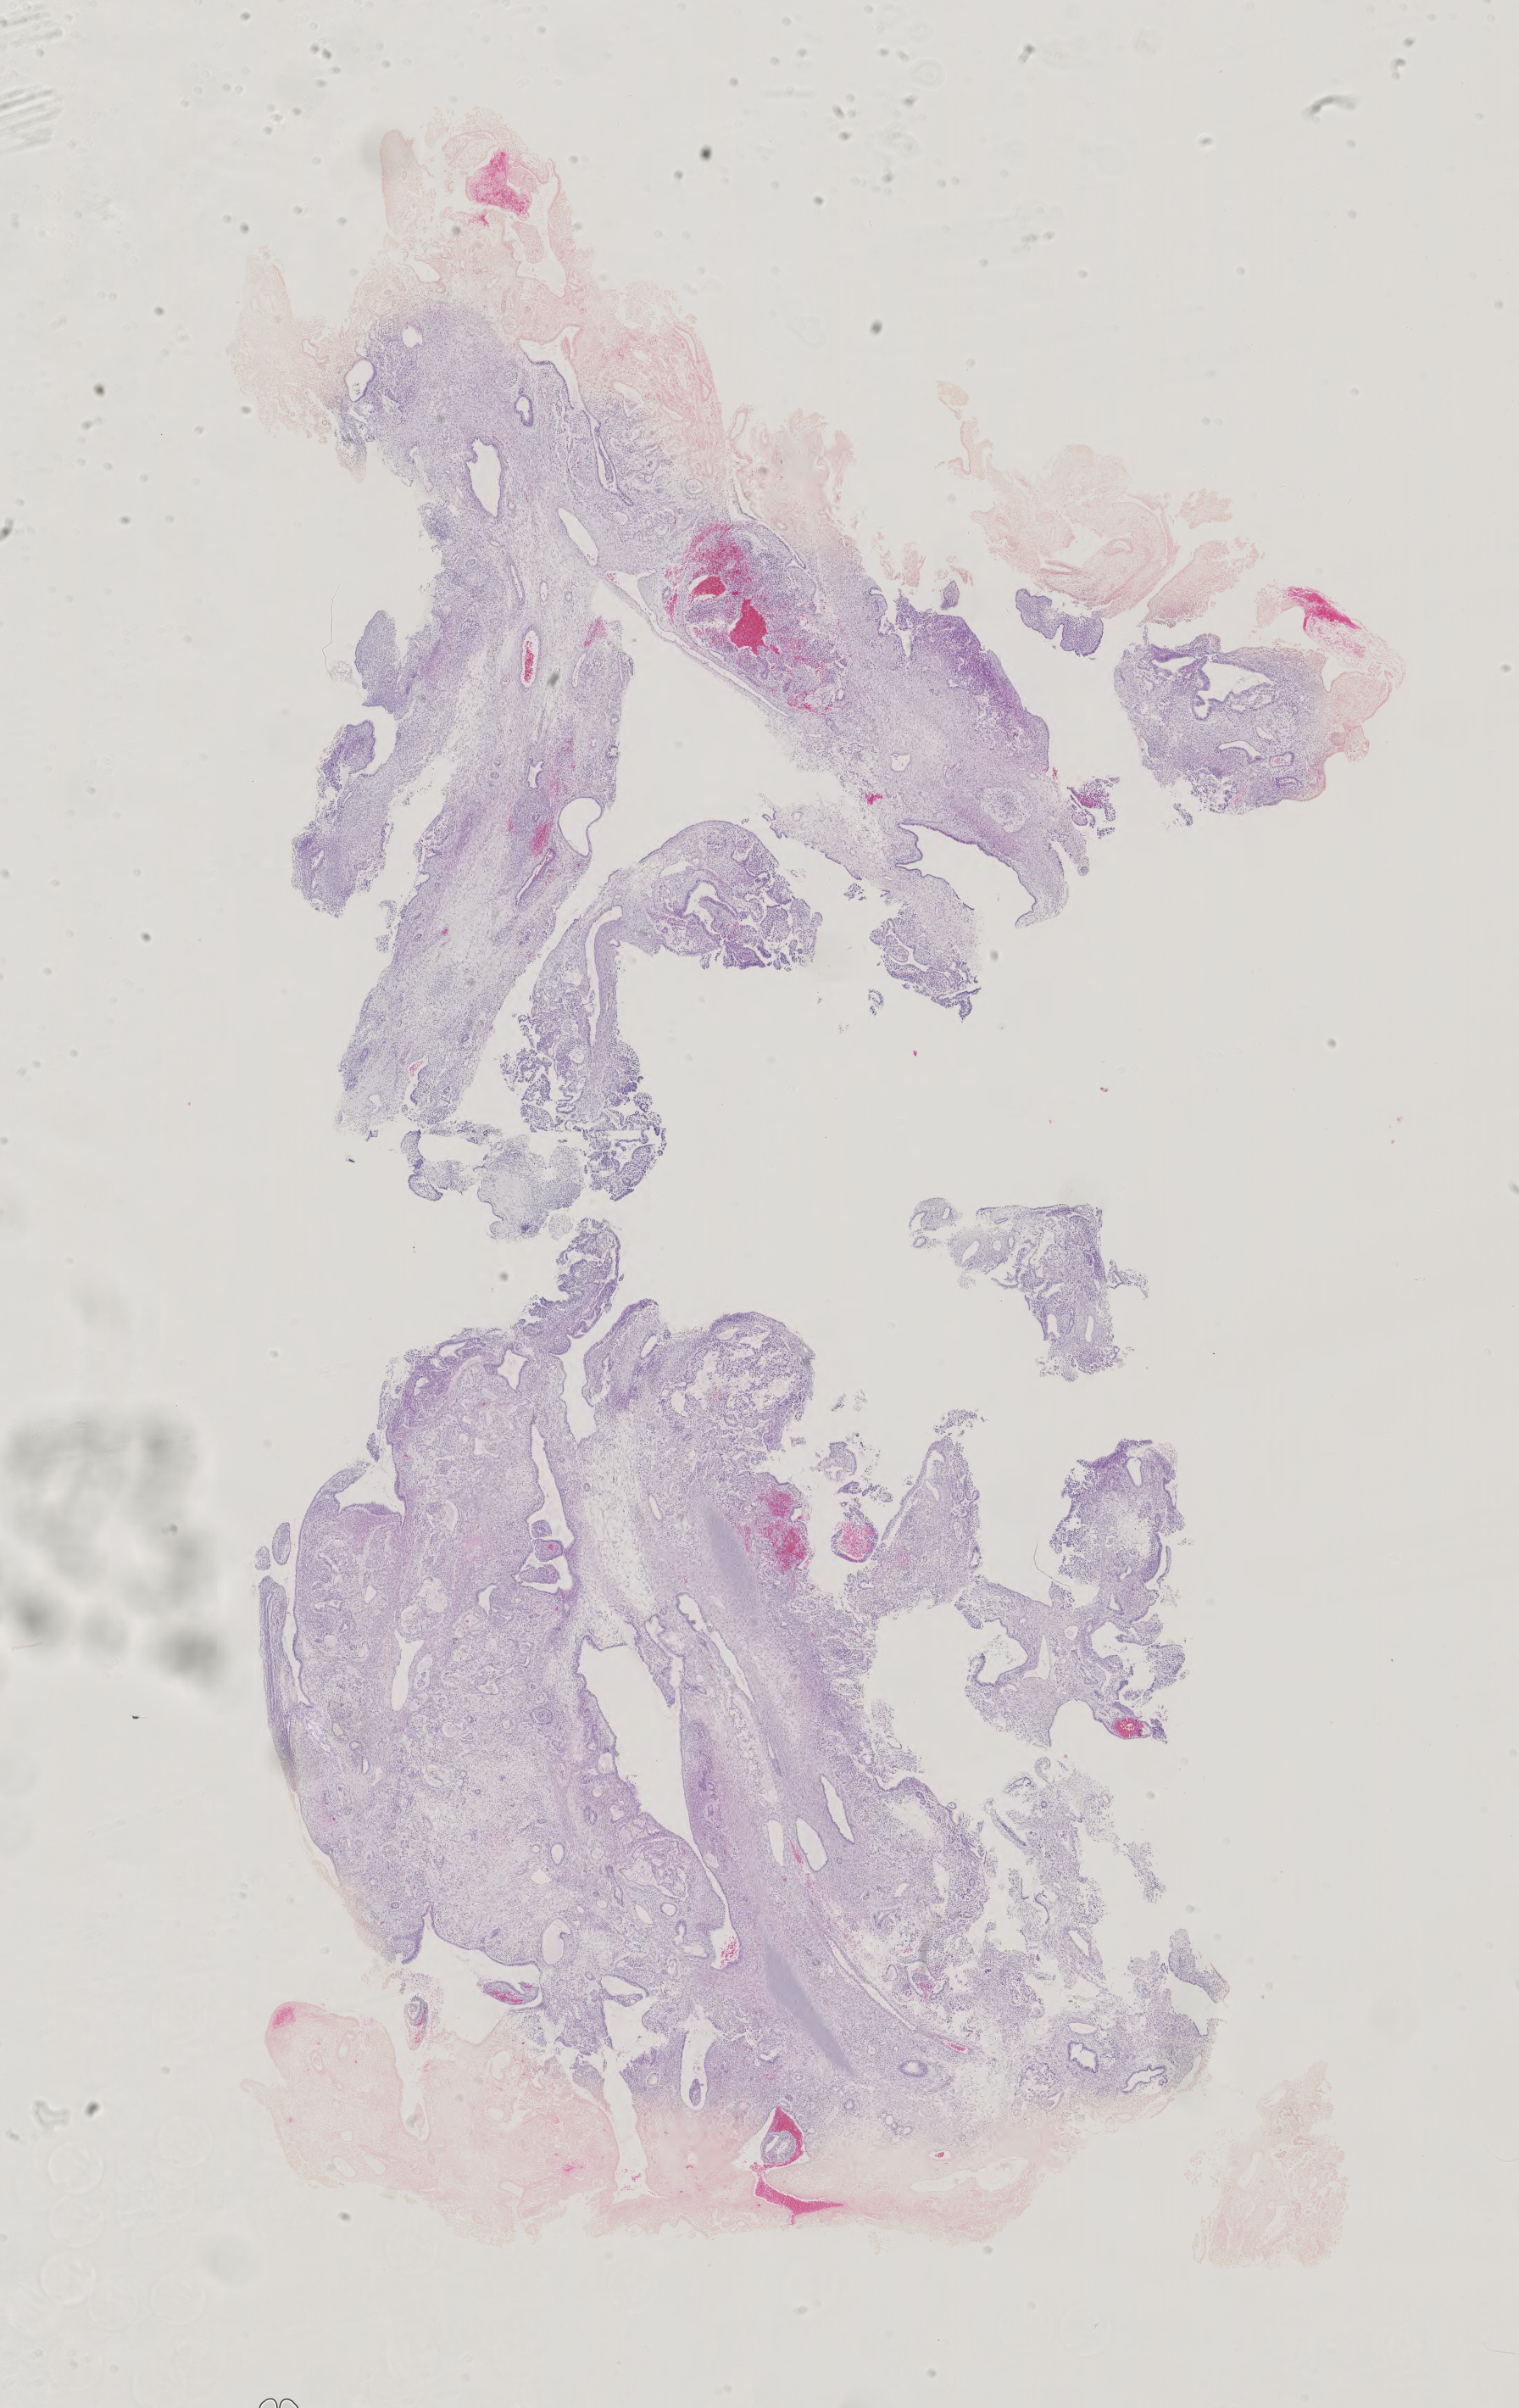
Digitized H&E tissue section (whole slide), a low-resolution overview of the entire scanned area, about 13.1 x 20.7 mm. Formalin-fixed paraffin-embedded (FFPE) diagnostic section. Sample: primary tumour, testis. Male, age 31 years at initial diagnosis.
- AJCC pathologic stage: I
- laterality: right
- histologic diagnosis: Mixed germ cell tumor